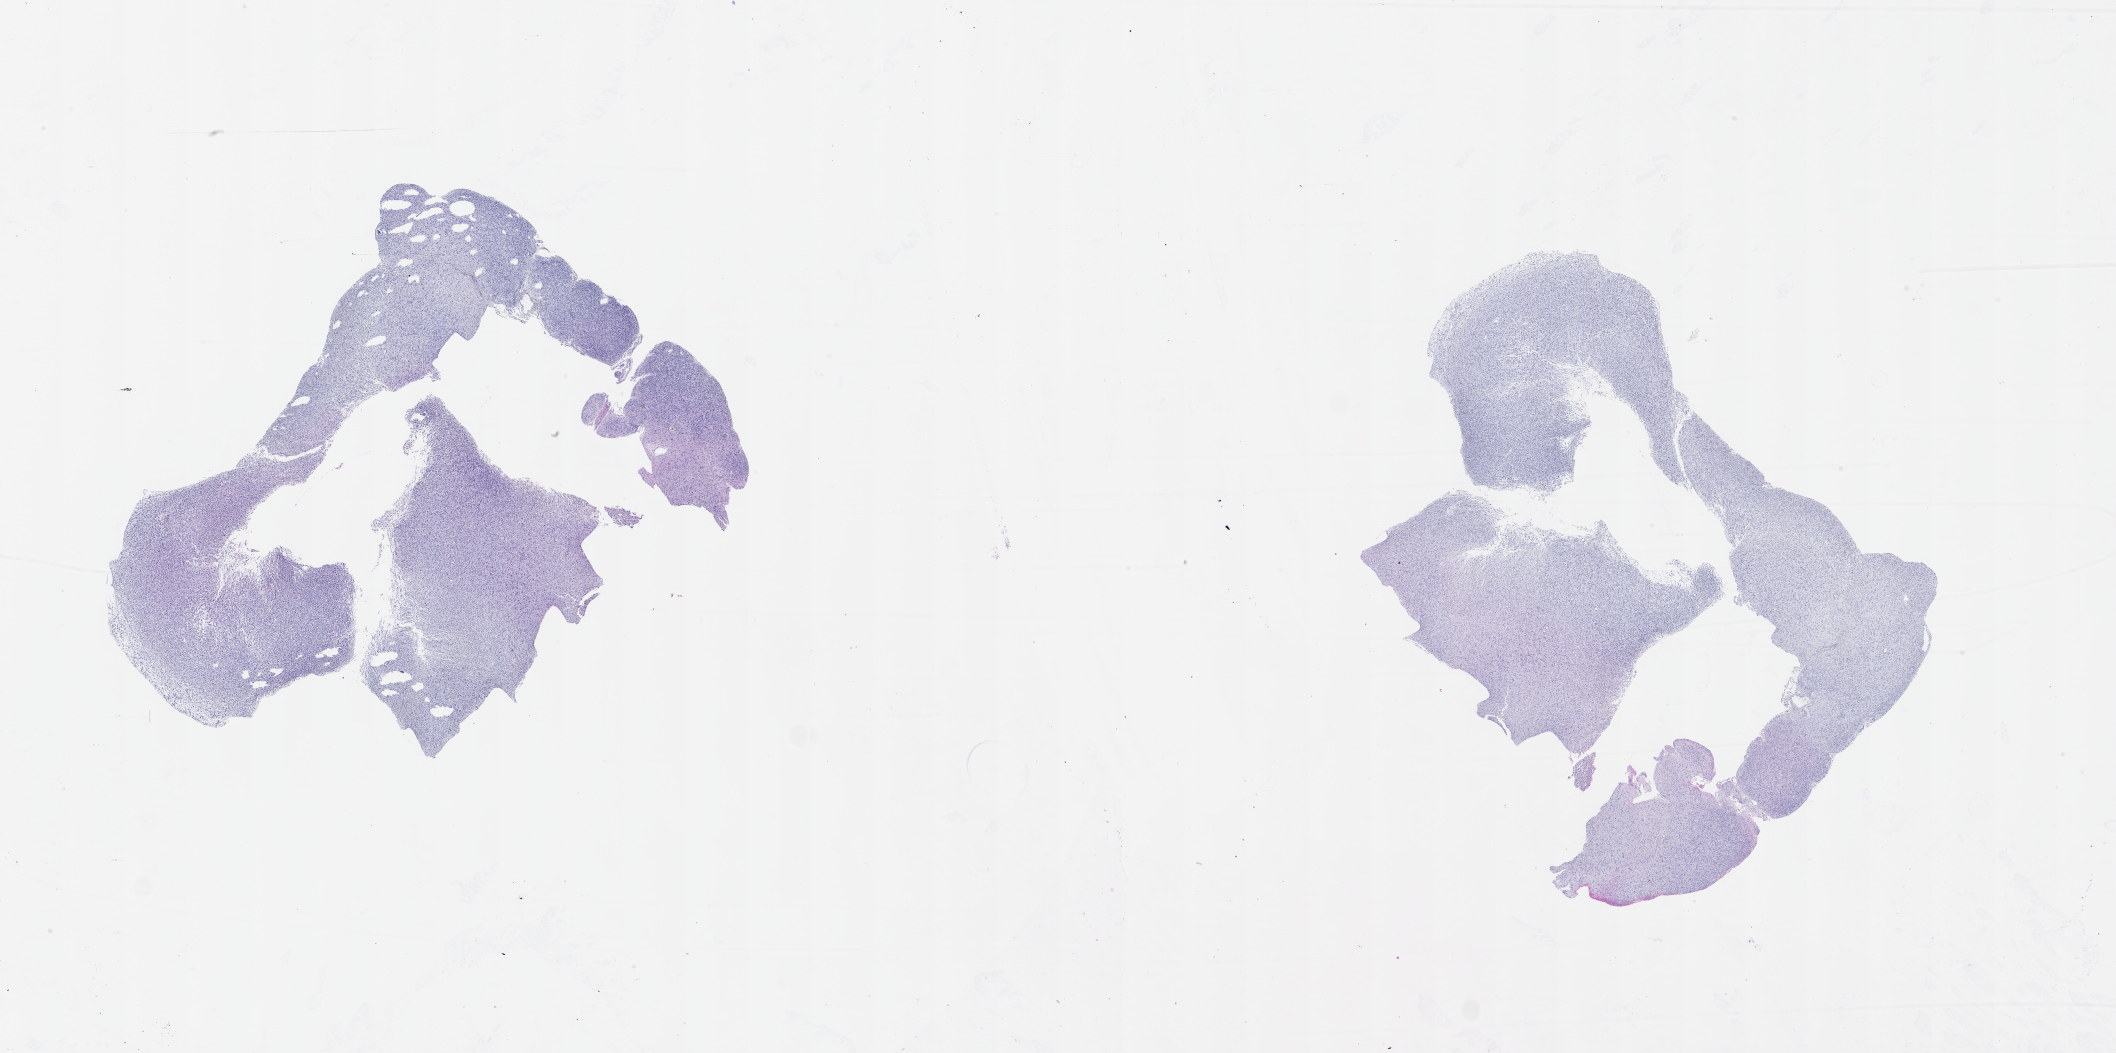
Whole-slide histology image, H&E — shown as a low-resolution overview of the whole scanned area (about 34.1 x 17.0 mm), brain, tumour tissue. 36-year-old male patient.
- primary tumour site (as recorded): frontal lobe
- diagnosis: Glioblastoma